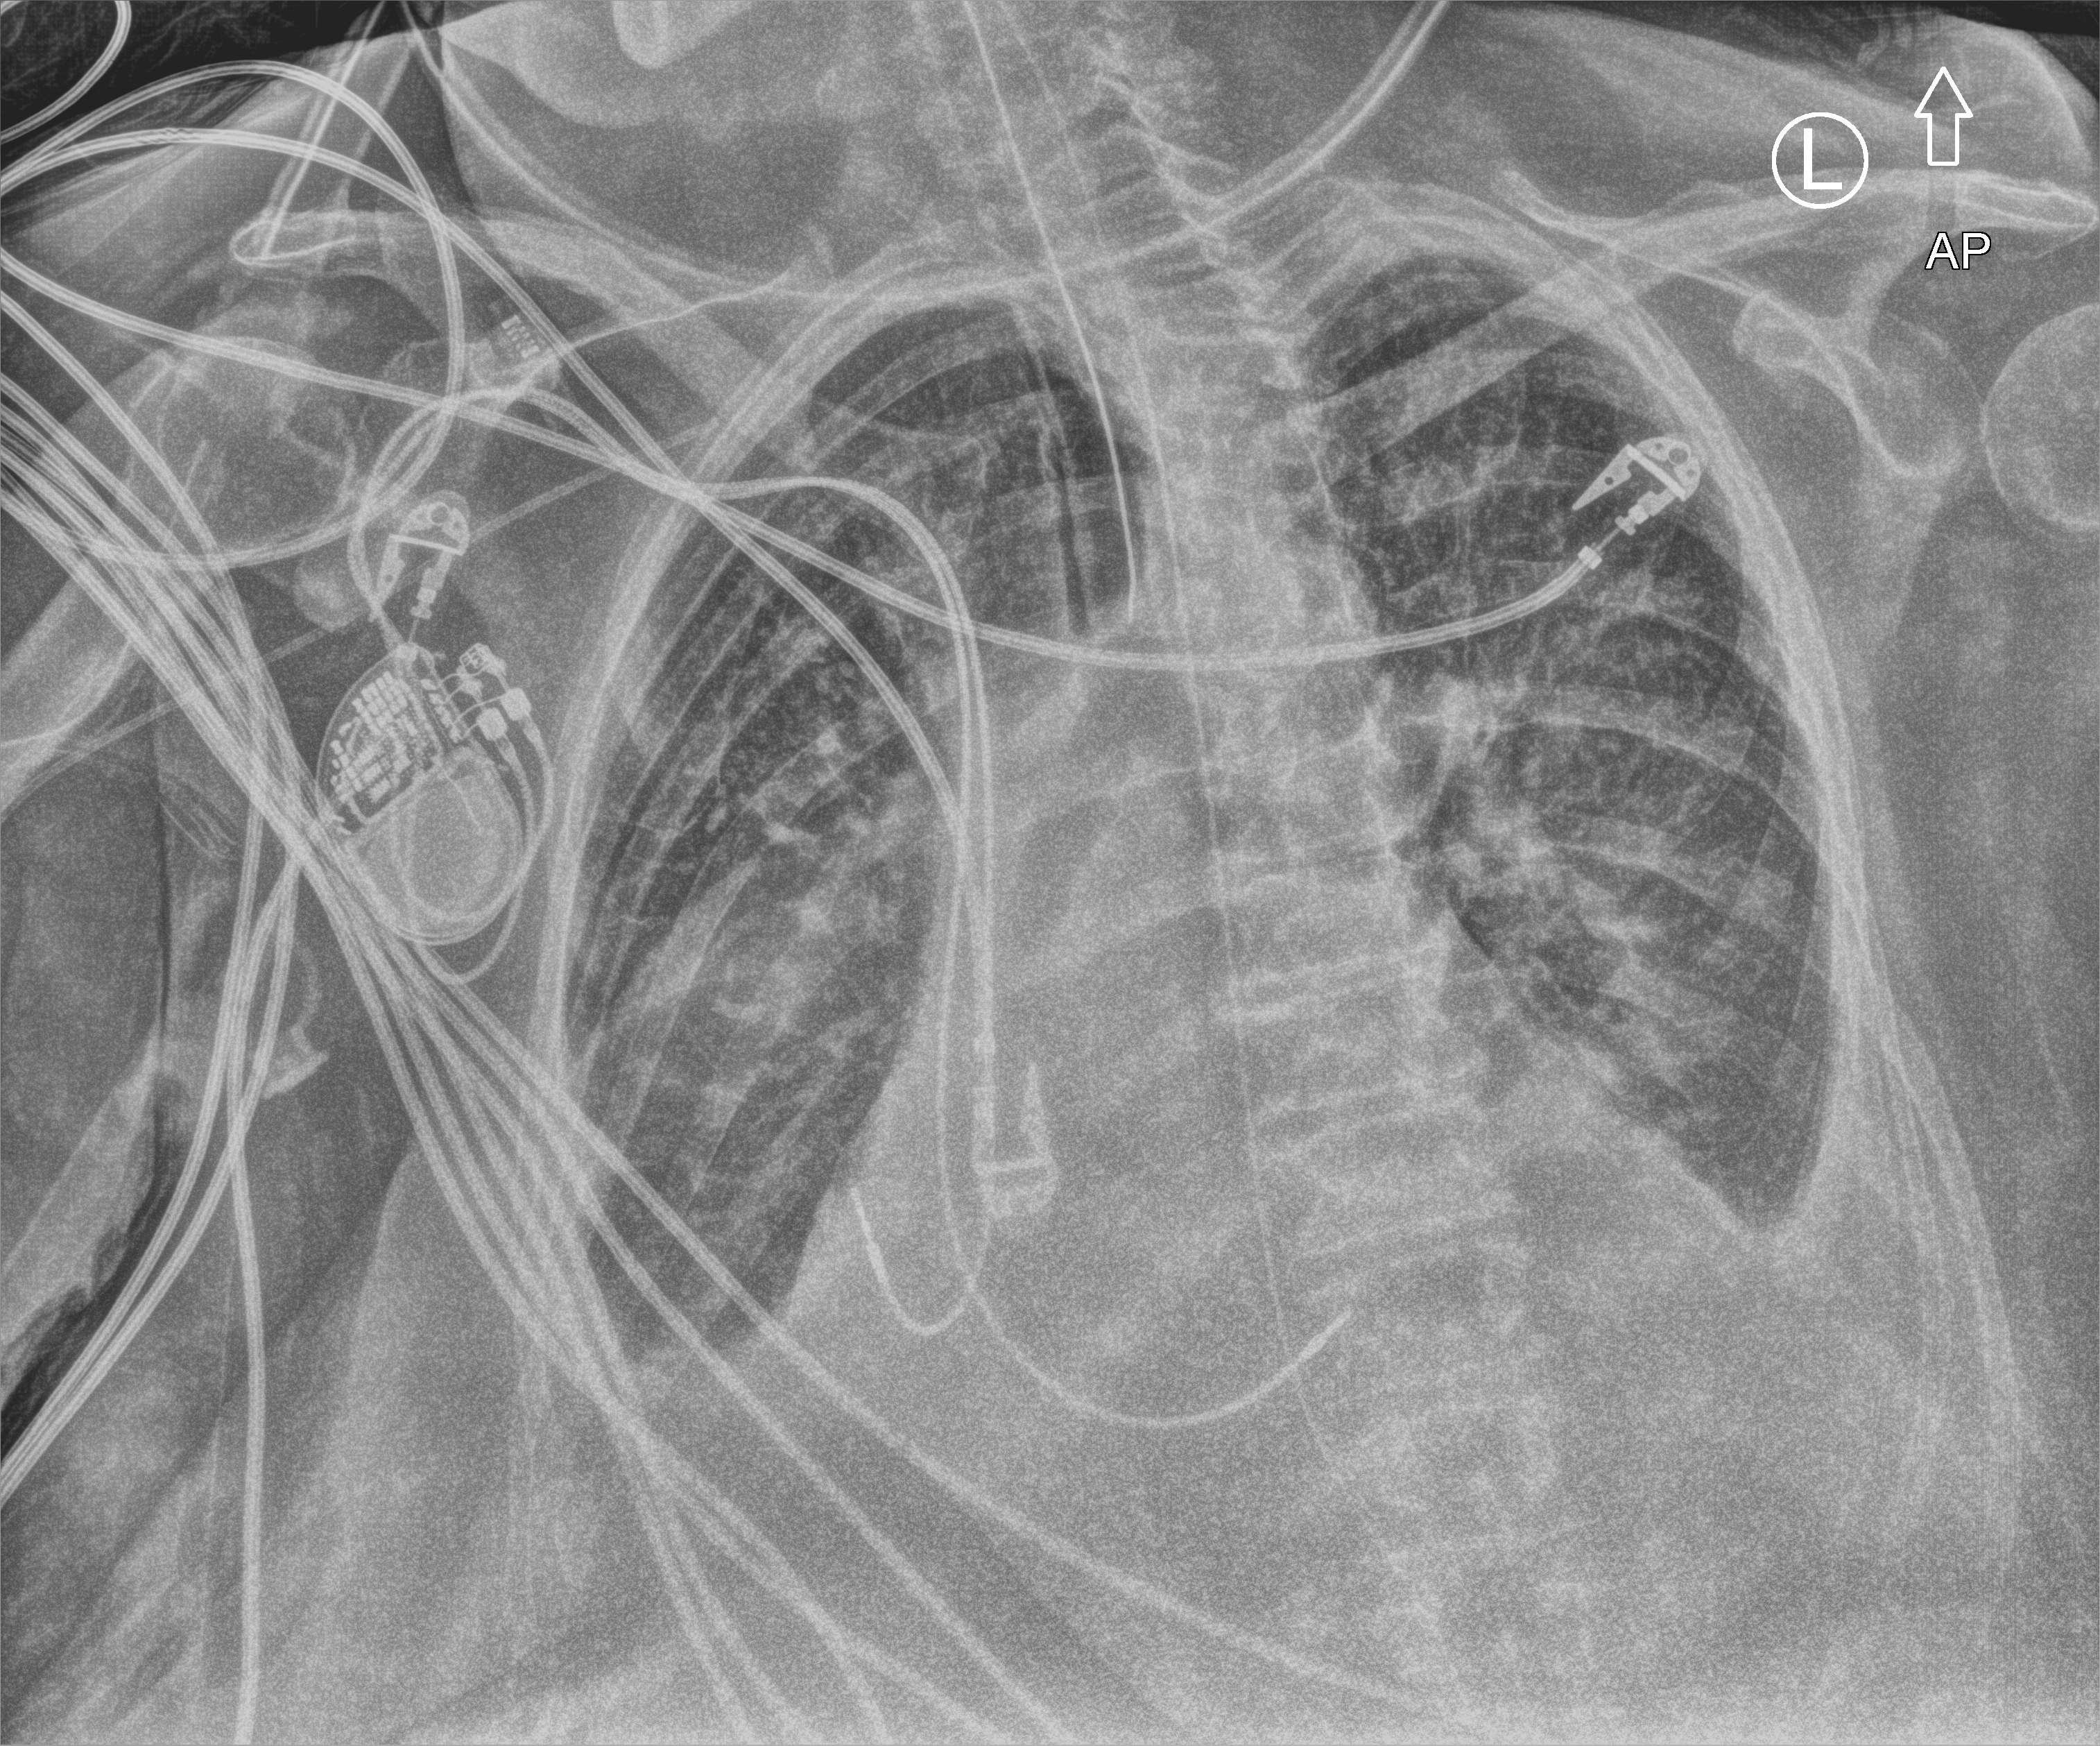
Chest X-ray (portable); anteroposterior (AP) projection. Female patient hospitalised with COVID-19, age 75–90 years.
From the hospital-stay record, not from the radiograph (when in the stay this image was taken is not recorded): admitted to intensive care during this hospital stay: yes.